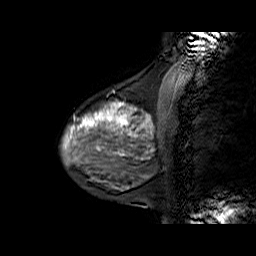
Breast MRI (dynamic contrast-enhanced), one sagittal slice; position 20 of 60 along the scan axis; dynamic contrast-enhanced series, time point 2 of 6 at this slice position (early post-contrast); 1.5 T; TE 6.3 ms, TR 32.9 ms; 4 mm slice thickness; 256 × 256 image matrix, field of view 200 × 200 mm. Female patient. From the clinical record (not read from this slice): setting: breast cancer imaged before/during neoadjuvant chemotherapy; receptor status: HR-positive, HER2-negative.
Outlined on this slice (semi-automatically segmented with operator editing):
- analysis volume of interest (the breast-tissue region the enhancement analysis was run in; not a lesion): bounding box (x1, y1, x2, y2) in pixels: (63, 86, 169, 170)
- tumour enhancement mask (voxels above the 100 % enhancement threshold inside the analysis volume of interest): (71, 102, 152, 149)